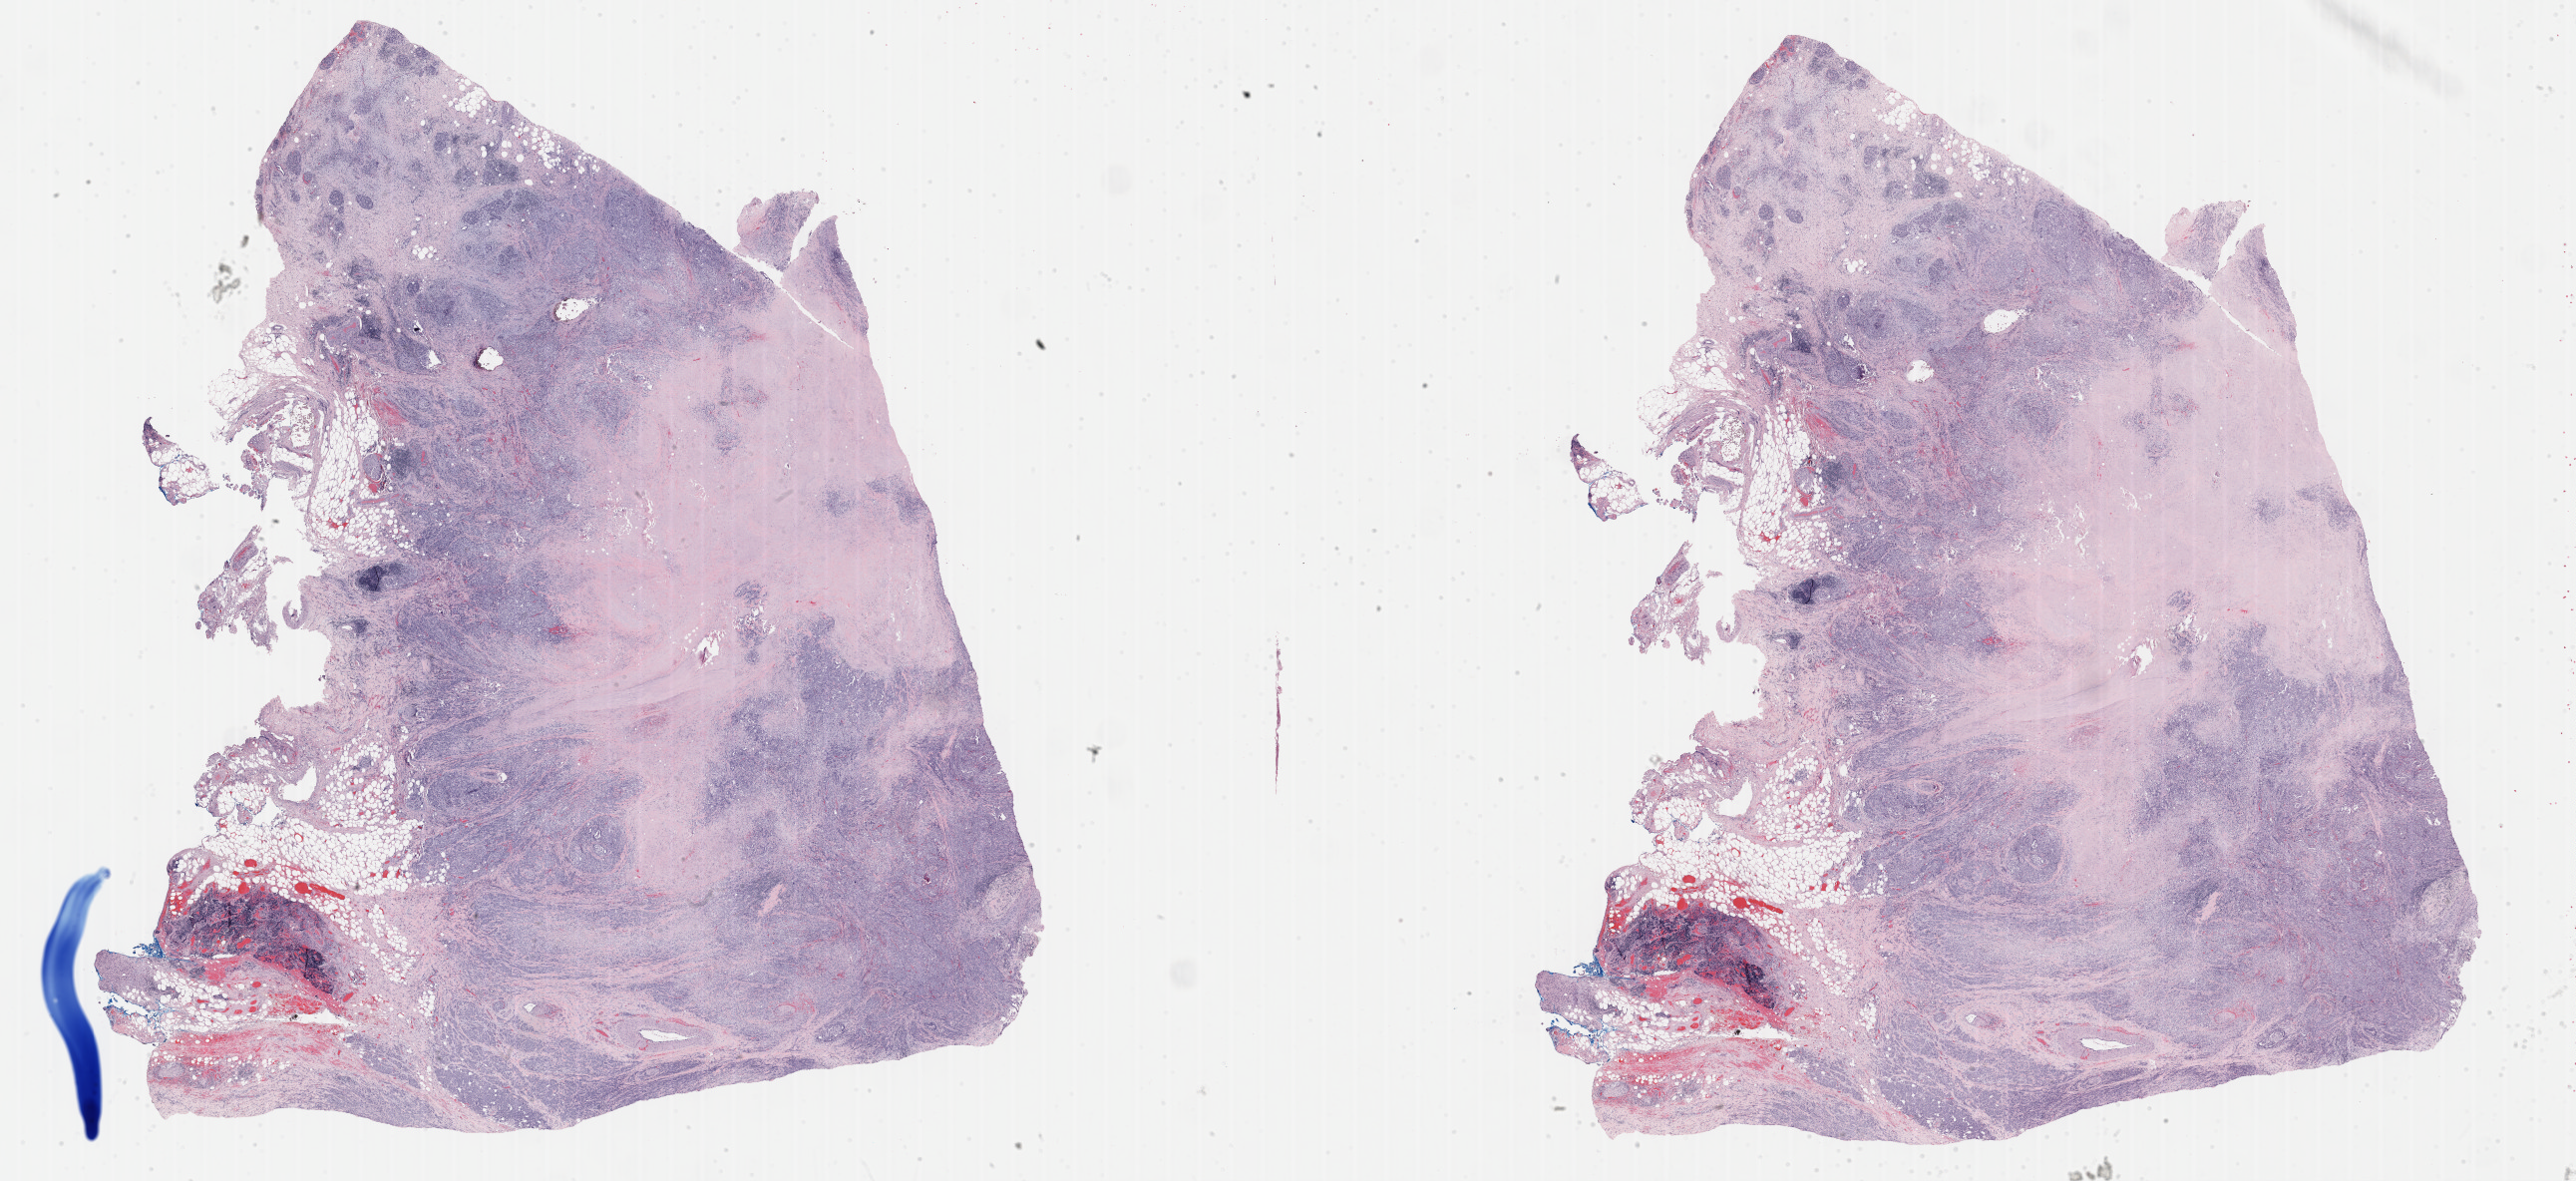
Digitized H&E-stained tissue section (whole slide), whole scanned area (about 41.8 x 19.2 mm) shown as a low-resolution overview, FFPE section, pancreas, primary tumour sample. Patient: female, age at initial diagnosis 48 years. Histologic grade: G3 (poorly differentiated).
AJCC pathologic stage: IIB (7th edition). Lymph nodes positive (case pathology): 2 of 11 examined. Pathologic diagnosis: Infiltrating duct carcinoma, NOS (head of pancreas). TNM: T3 N1 M0.